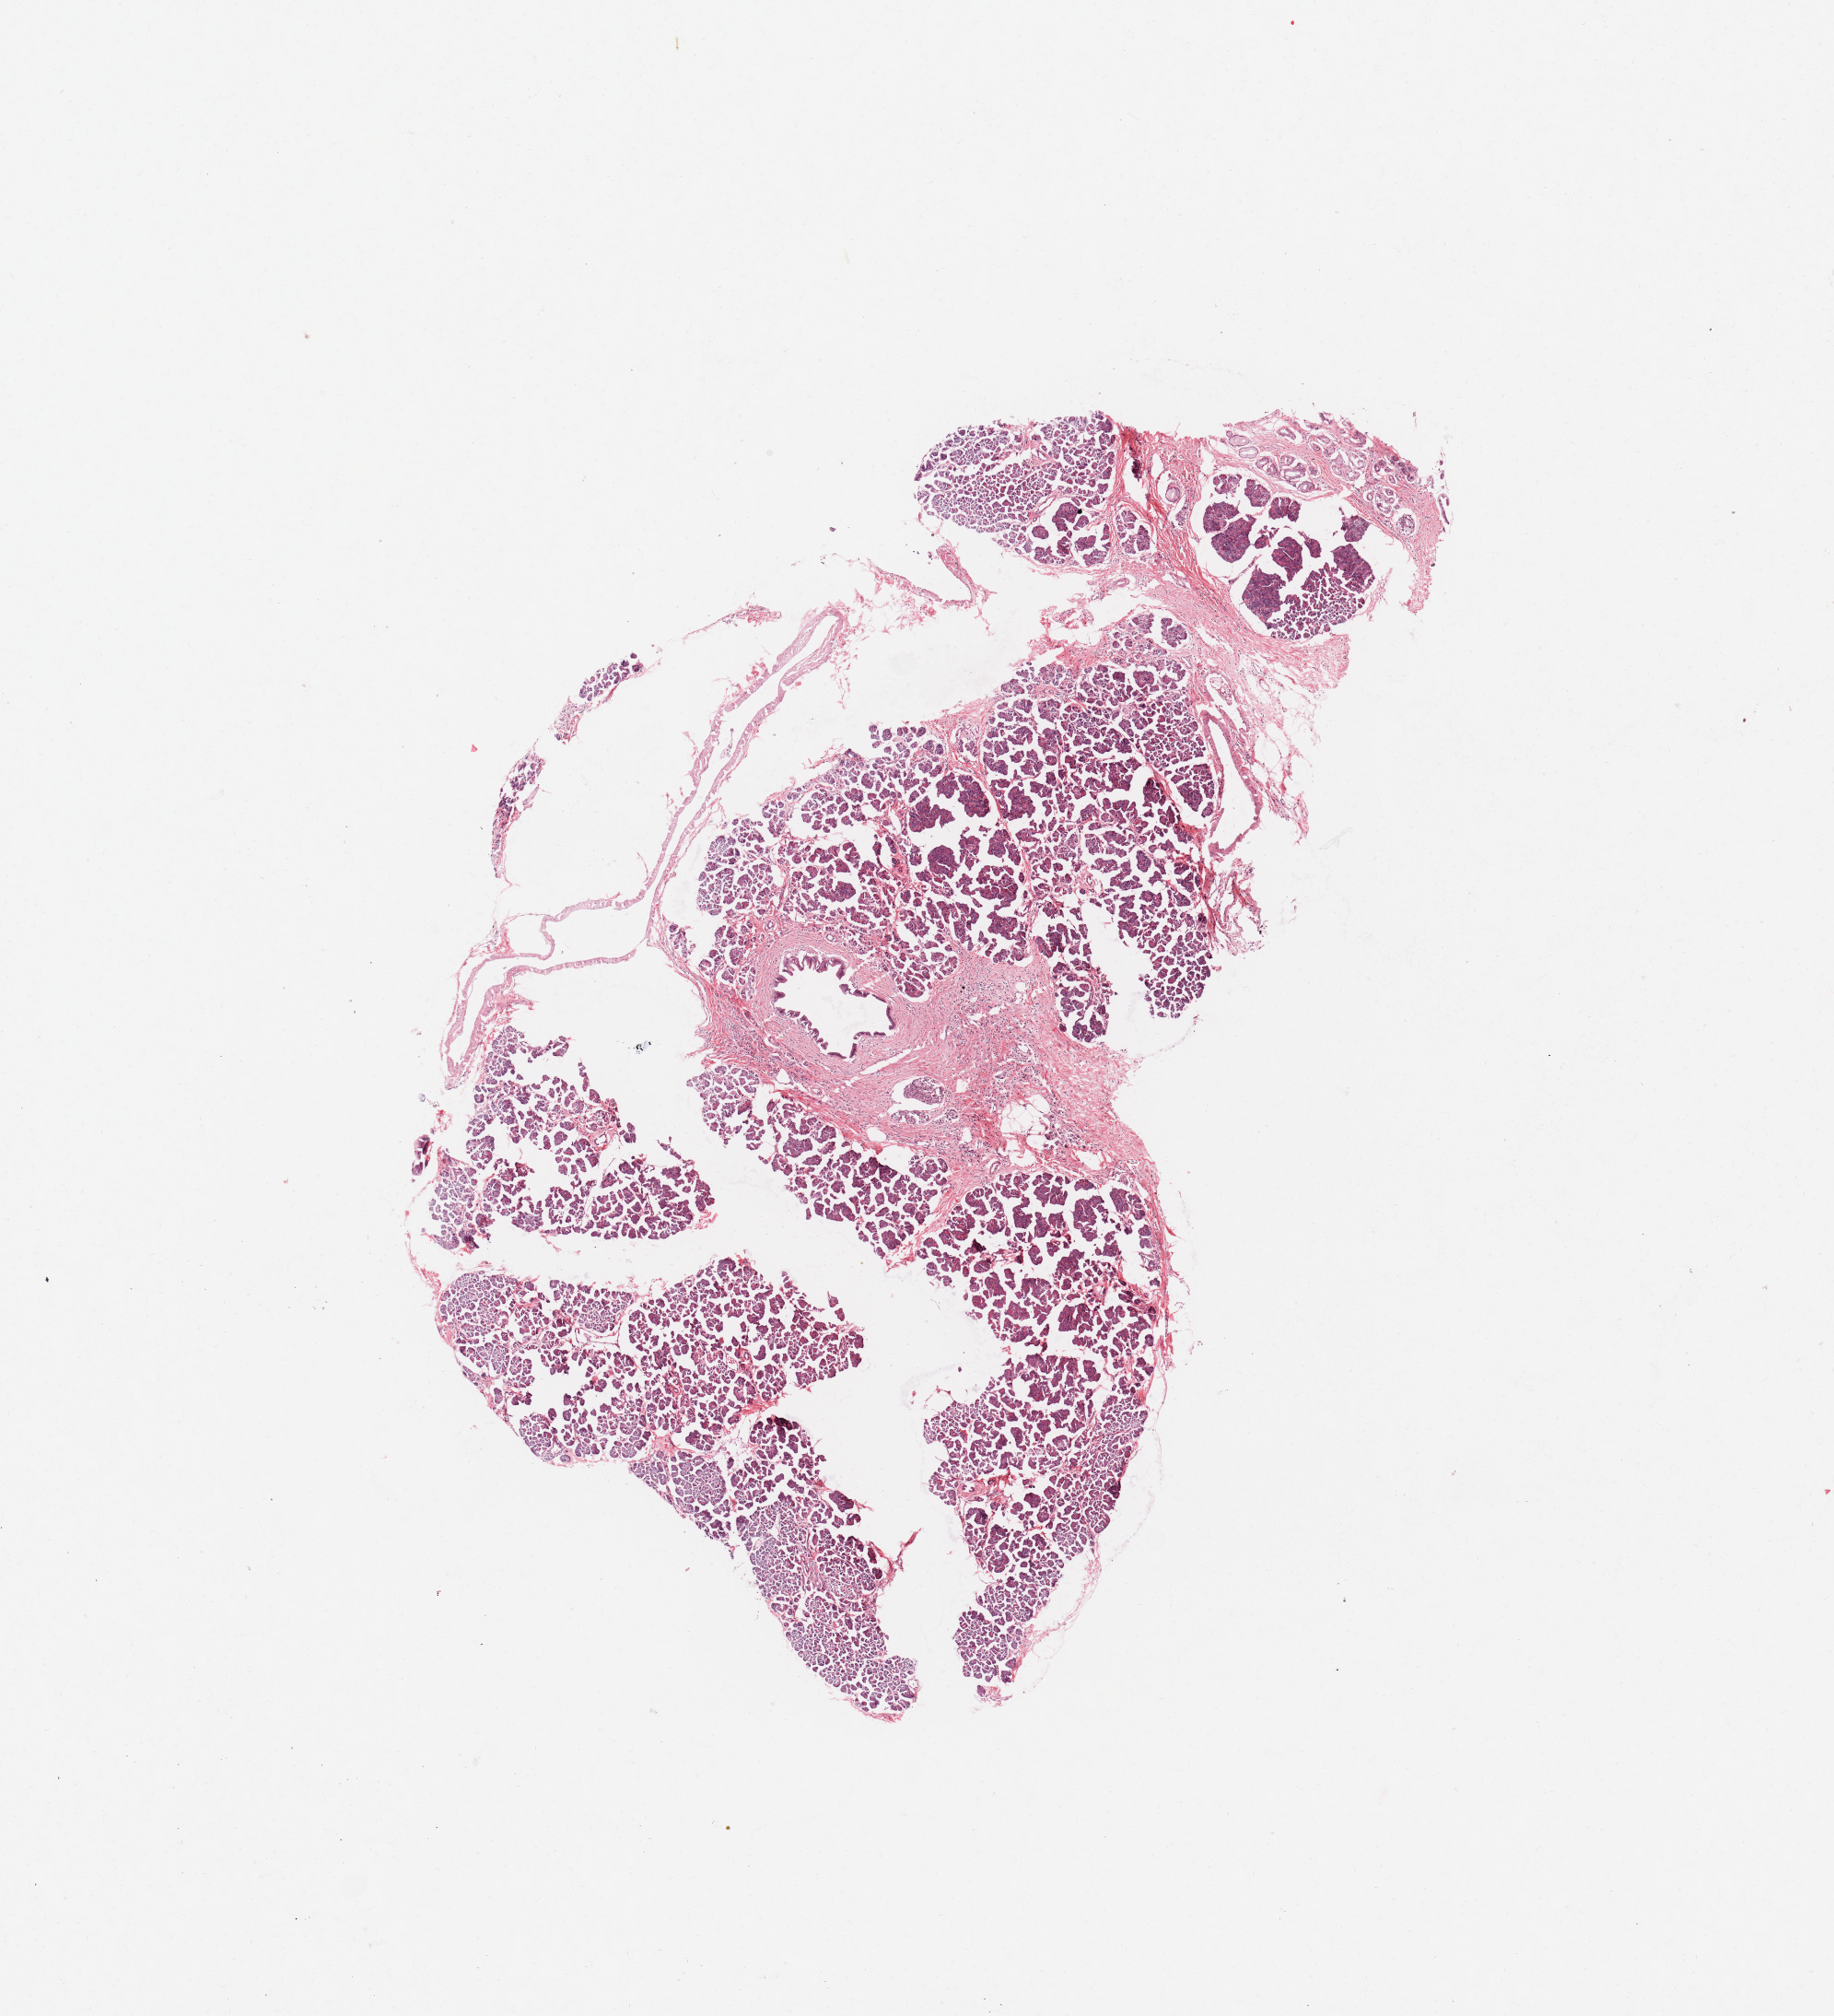
Digitized H&E tissue section (whole slide) — low-resolution overview of the scanned area, about 7.9 x 8.7 mm. Normal (non-tumour) tissue sample, pancreas. Female, 54 y/o.
* this section: normal (non-tumour) tissue from the same patient
* patient diagnosis: Infiltrating duct carcinoma, NOS